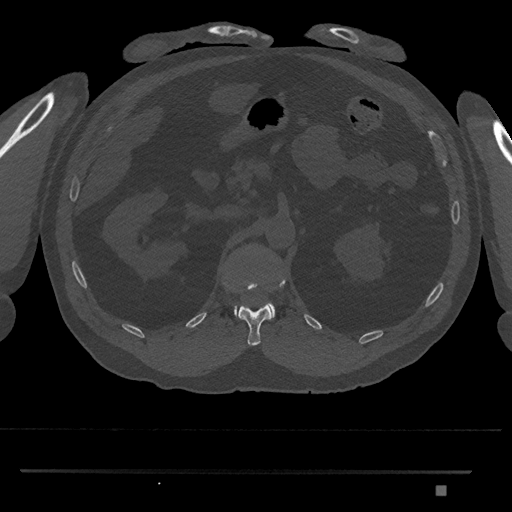
CT including the spine, one axial slice. Slice 864 of 1134 in the series (ordered by position). Reconstruction kernel Br40s/3. 120 kVp. Bone window (W 1800 / L 400 HU). 512 × 512 image matrix, field of view 429 × 429 mm. Male patient, age 65 years. From the clinical record (not read from this slice): primary cancer: prostate.
Annotated regions visible in this slice (semi-automatic segmentation, software-assisted and operator-edited):
- L1 vertebra: box from (x=234, y=249) to (x=275, y=319) px
- T12 vertebra: (x=224, y=278)–(x=285, y=346)